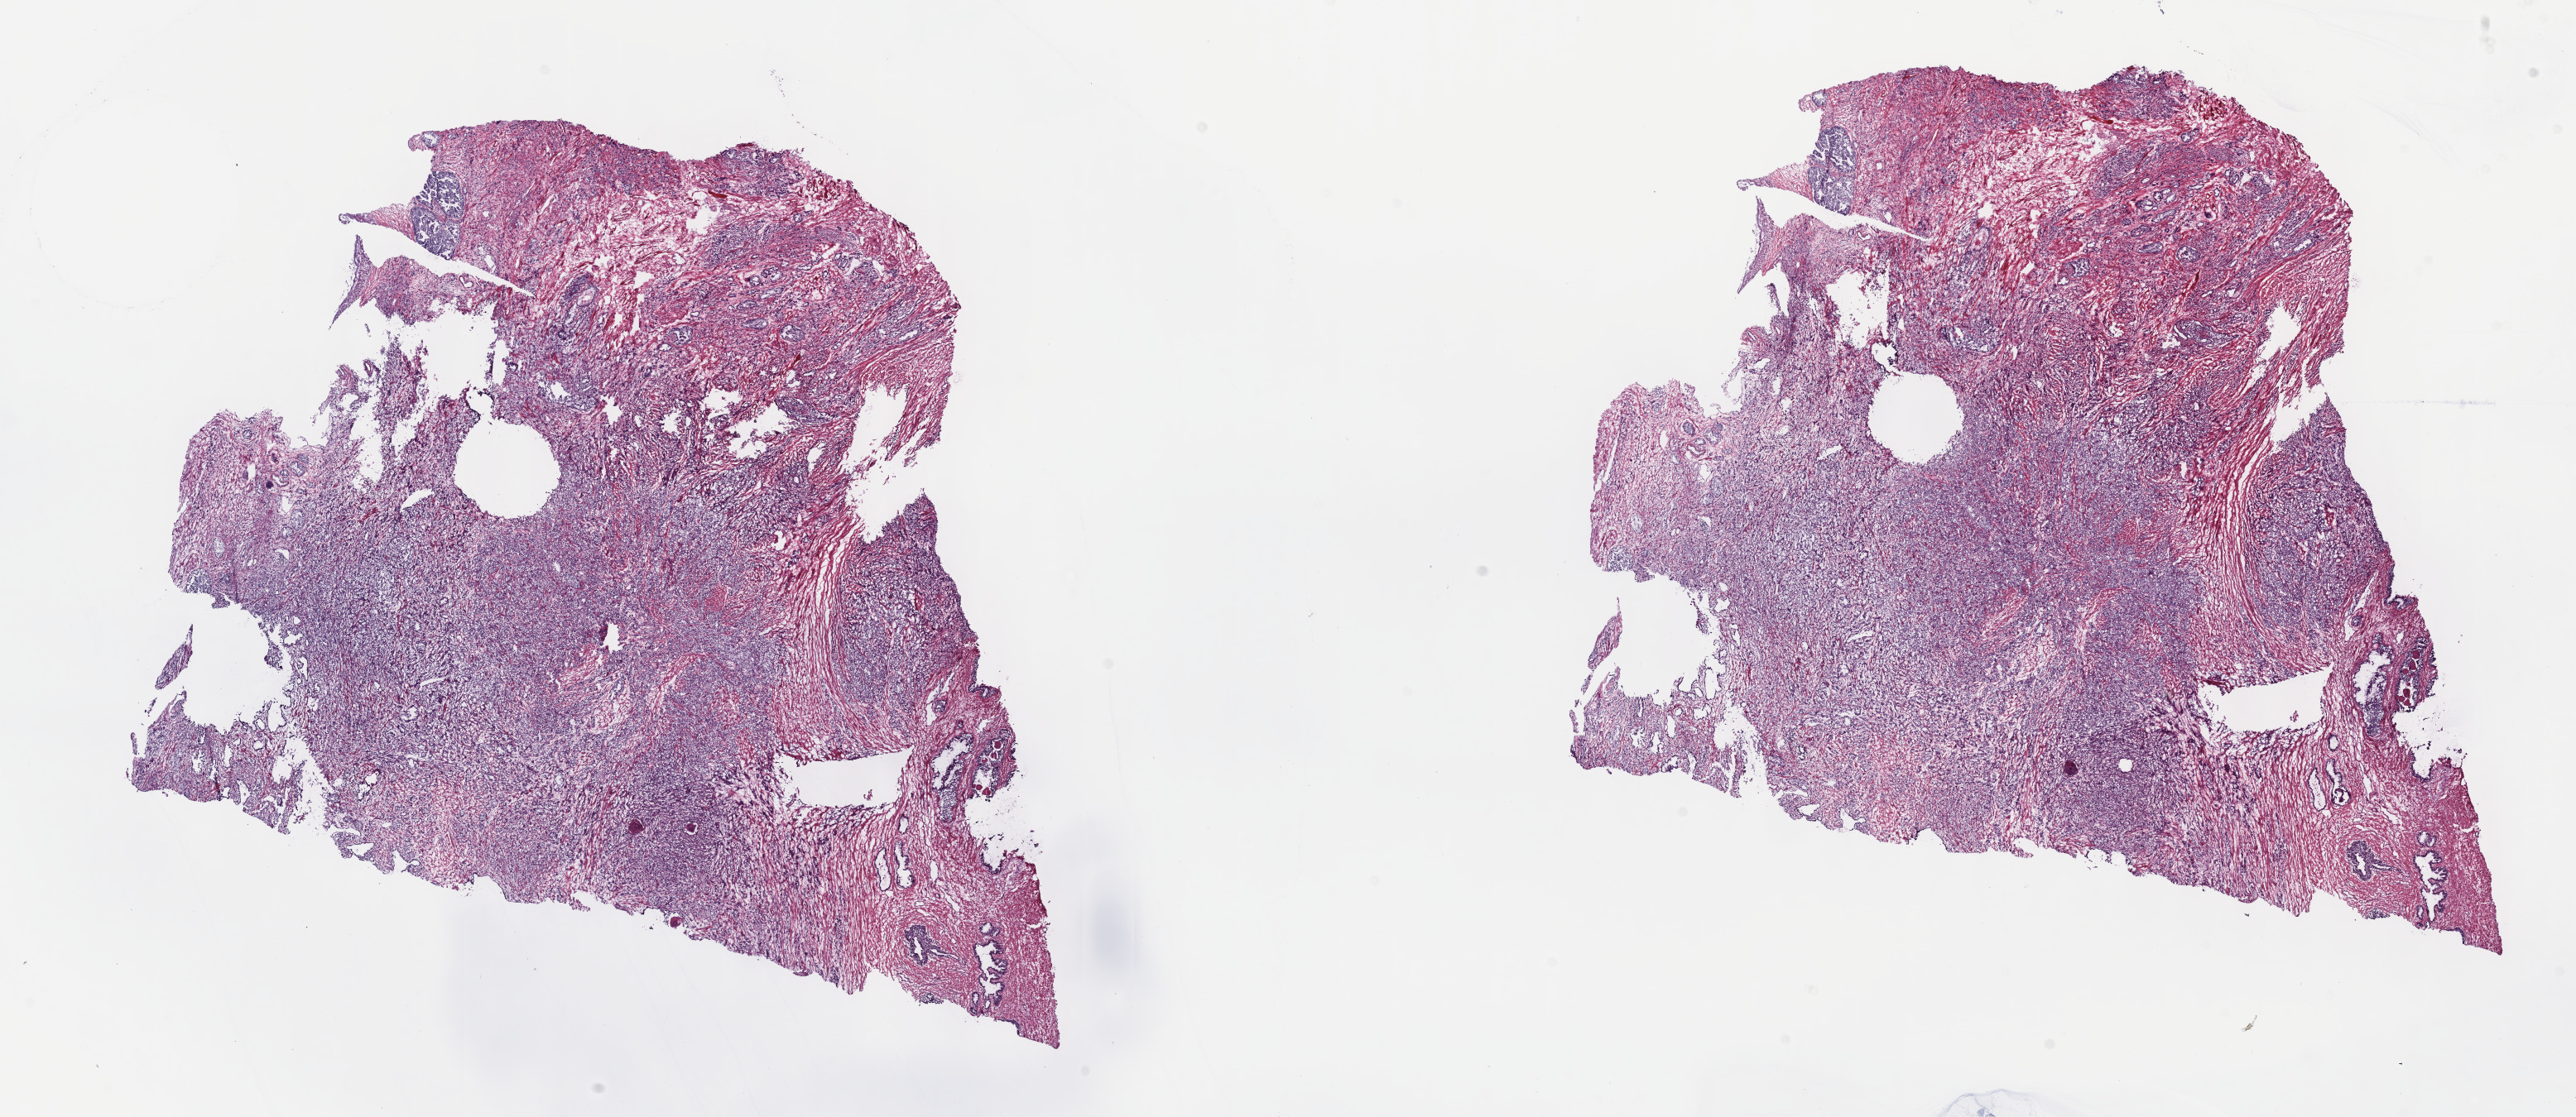
Whole-slide histology image, H&E, whole scanned area (about 25.2 x 10.9 mm) shown as a low-resolution overview, frozen section, prostate, primary tumour sample. Male patient; age at initial diagnosis 70 years. Gleason score: 9 (5+4). Pathologist review of this section (percent, as recorded): tumour cells 60%, tumour nuclei 75%, normal cells 10%, stromal cells 30%, necrosis 0%. Inflammatory infiltration, as recorded: lymphocyte infiltration 0%, monocyte infiltration 0%, neutrophil infiltration 0%.
* lymph nodes positive (case pathology): 0 of 5 examined
* histologic diagnosis: Adenocarcinoma, NOS (prostate gland)
* laterality: bilateral